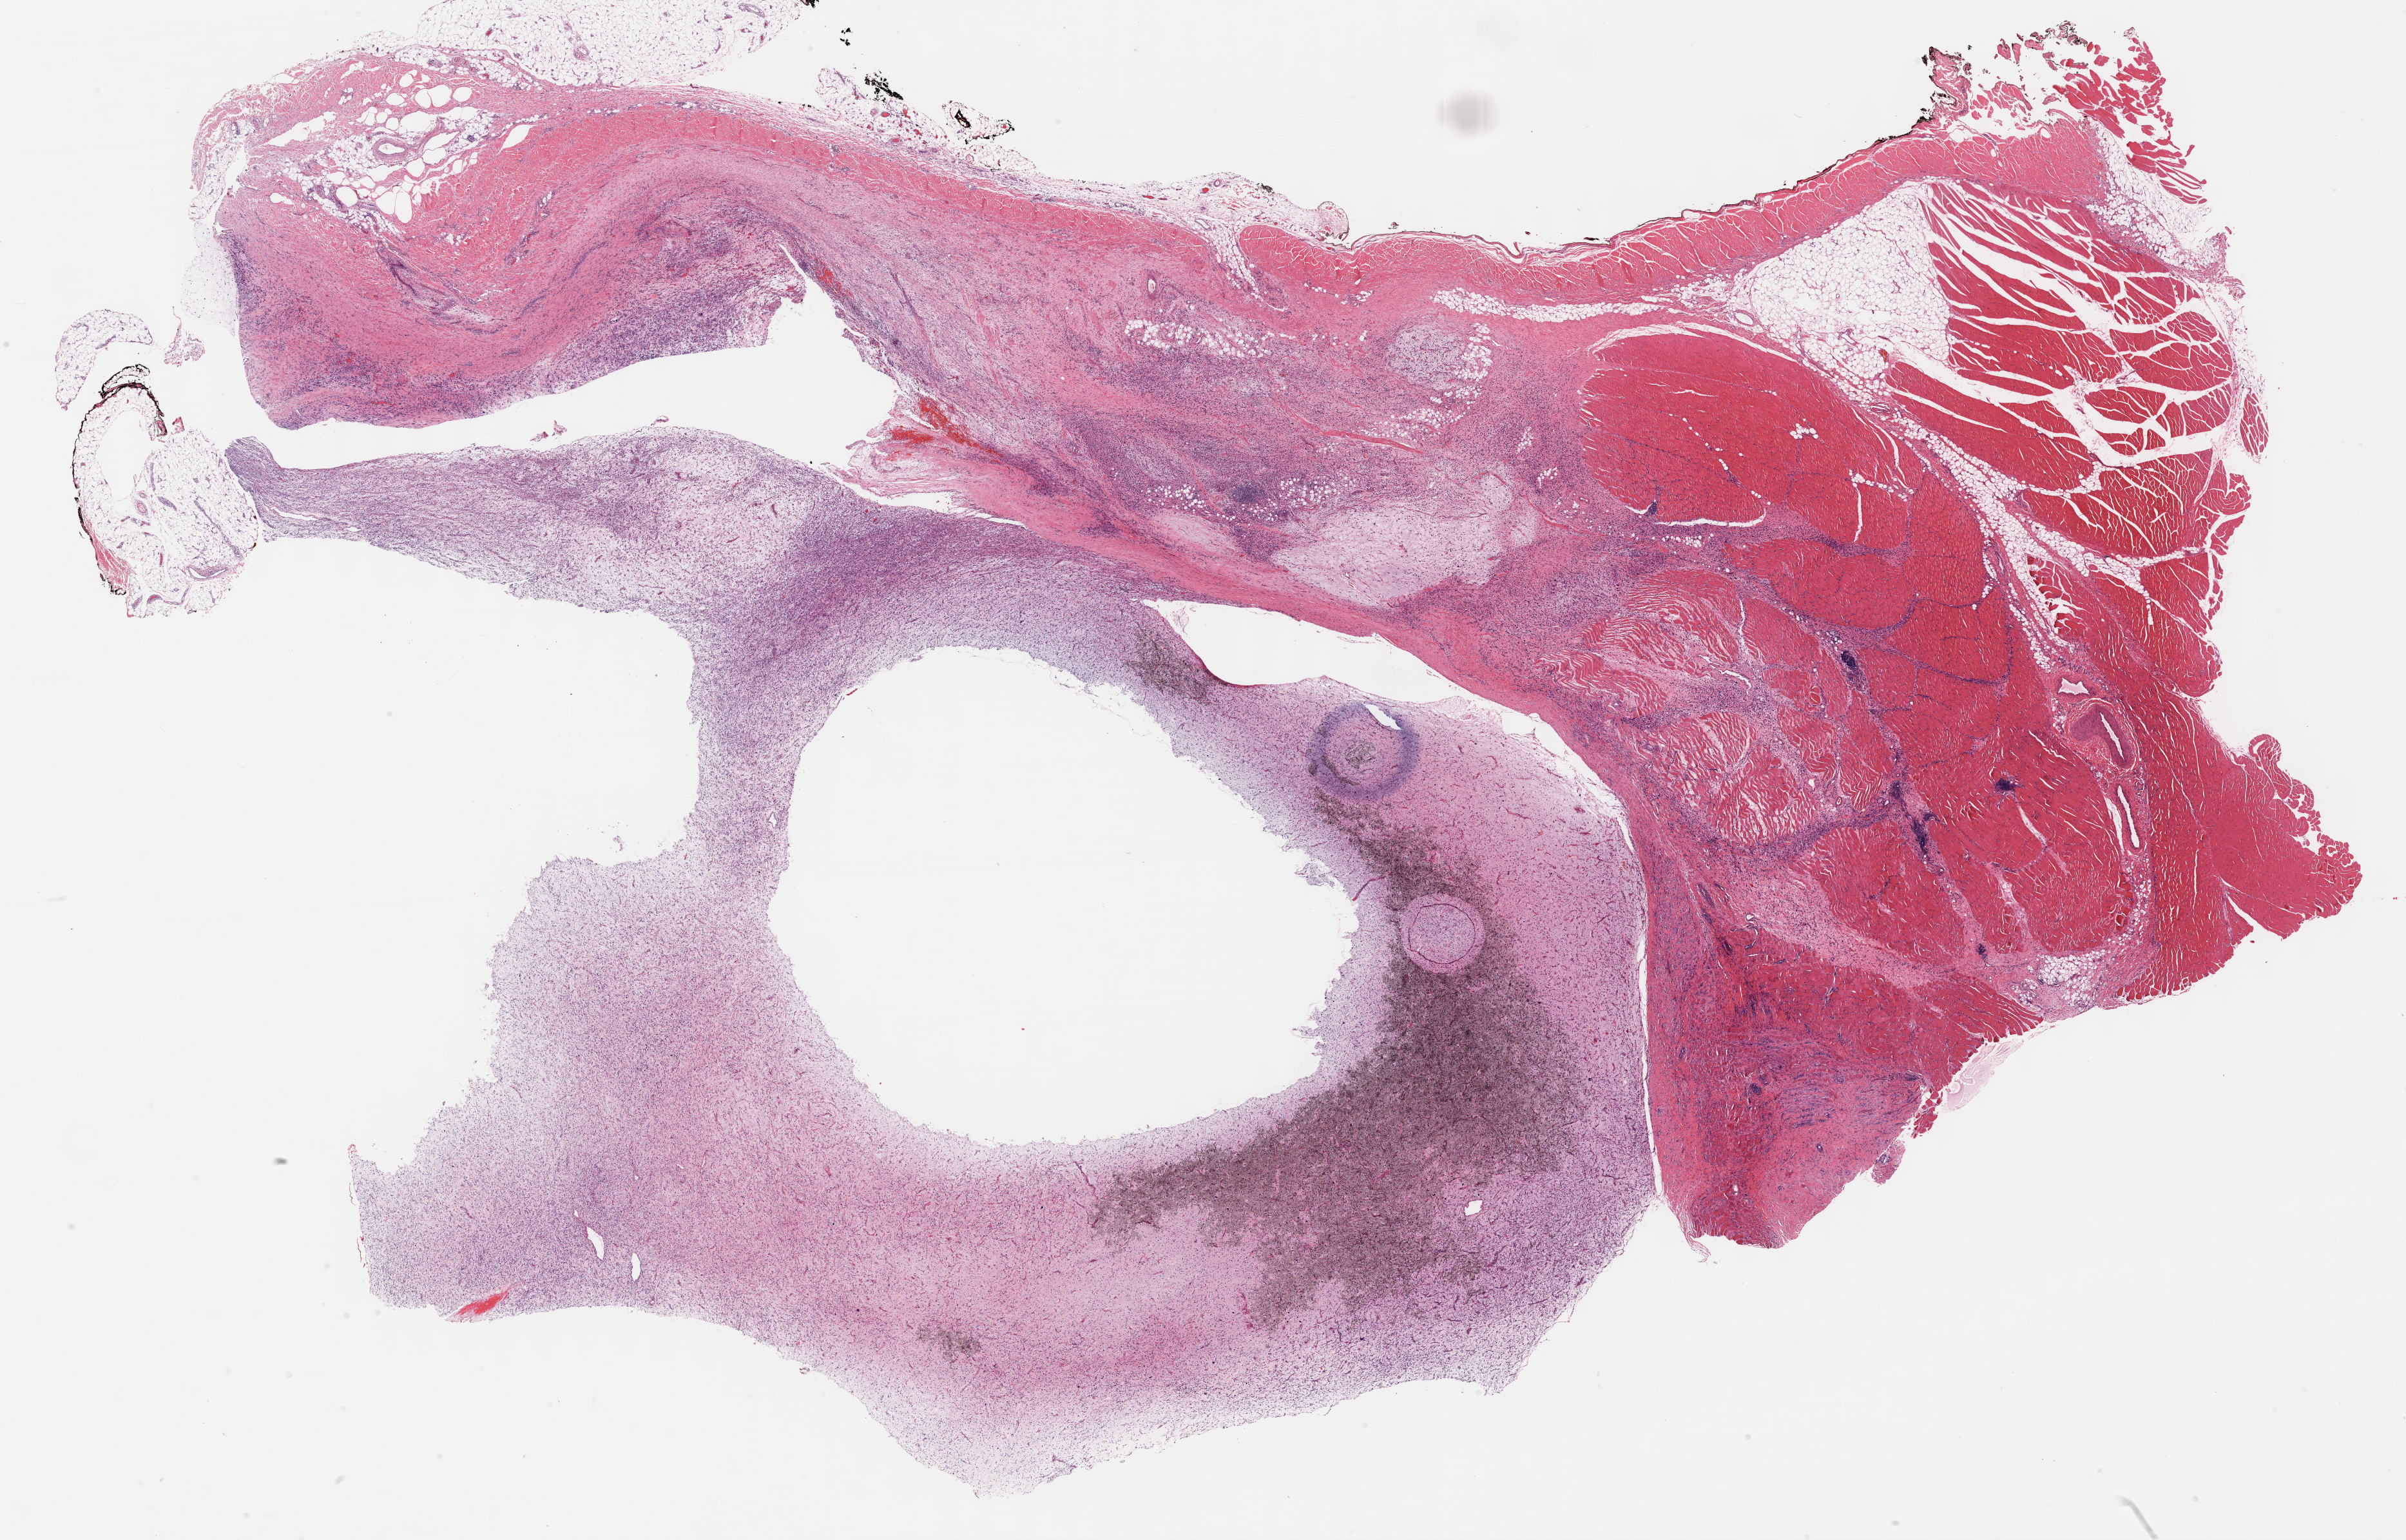
Digitized H&E-stained tissue section (whole slide), shown as a low-resolution overview of the whole scanned area (about 30.2 x 19.3 mm, slide scanned at 40x); formalin-fixed paraffin-embedded (FFPE) diagnostic section; connective, subcutaneous and other soft tissues, primary tumour sample. Male, age 35 years at initial diagnosis.
• histologic diagnosis: Fibromyxosarcoma (connective, subcutaneous and other soft tissues of lower limb and hip)